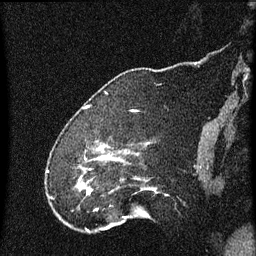
Breast MRI (dynamic contrast-enhanced), one sagittal slice. Position 15 of 60 along the scan axis. Dynamic contrast-enhanced series, image 2 of 4 at this slice position (ordered by acquisition). 1.5 T. TE 4.2 ms, TR 8 ms. 256 × 256 image matrix, field of view 180 × 180 mm. Female patient, age 52 years.
Outlined on this slice (semi-automatic segmentation, software-assisted and operator-edited):
- analysis volume of interest (the breast-tissue region the enhancement analysis was run in; not a lesion): bounding box (x1, y1, x2, y2) in pixels: (76, 148, 166, 219)
- tumour enhancement mask (voxels above the 70 % enhancement threshold inside the analysis volume of interest): (80, 158, 113, 193)